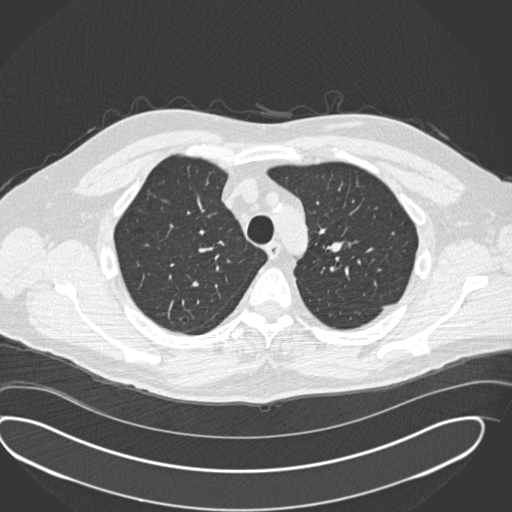
Axial slice from a low-dose chest CT screening exam; second screening round (one year after baseline); lung window (W 1500 / L -600 HU); 2 mm slice thickness; standard (soft-tissue) reconstruction kernel (B30f); slice 48 of 190 in the series; 512 × 512 image matrix. Male, age 56 years at enrolment.
• Expert reader's lesion annotation, bounding box (x1, y1, x2, y2) in pixels: (312, 225, 368, 271).
• No non-calcified nodule or mass ≥4 mm was recorded by the screening reader at this exam.
• Participant outcome: lung cancer diagnosed 520 days after this screen — neuroendocrine carcinoma, NOS, left upper lobe, well differentiated (G1), stage IA (AJCC 6th edition), 20 mm at pathology.